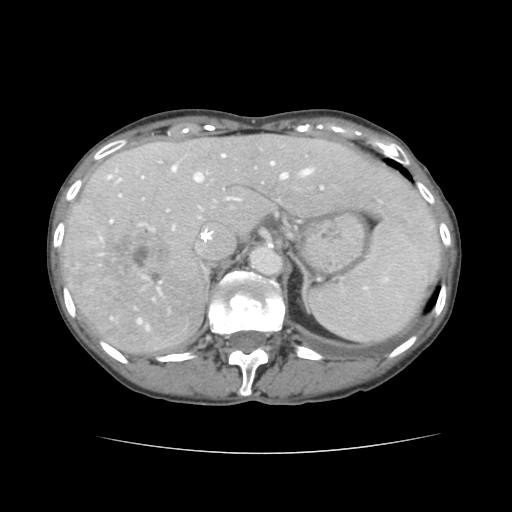
Contrast-enhanced abdominal CT, one axial slice. Position 102 of 136 along the scan axis. 120 kVp. Intravenous contrast given. Soft-tissue window (W 400 / L 40 HU). 2.5 mm slice thickness. 512 × 512 image matrix, field of view 319 × 319 mm. Female patient, age 77 years. From the clinical record (not read from this slice): diagnosis: colorectal cancer liver metastases, imaged before liver resection; multiple liver metastases: yes; largest metastasis: 3 cm.
Structures marked on this image (expert manual segmentation):
- hepatic veins: bounding box <108,154,311,329> (left, top, right, bottom; pixels)
- liver: <64,136,440,356>
- planned liver remnant (the part of the liver to remain after resection): <159,135,440,264>
- portal vein (with intrahepatic branches): <110,170,383,283>
- liver metastasis: <103,226,177,296>